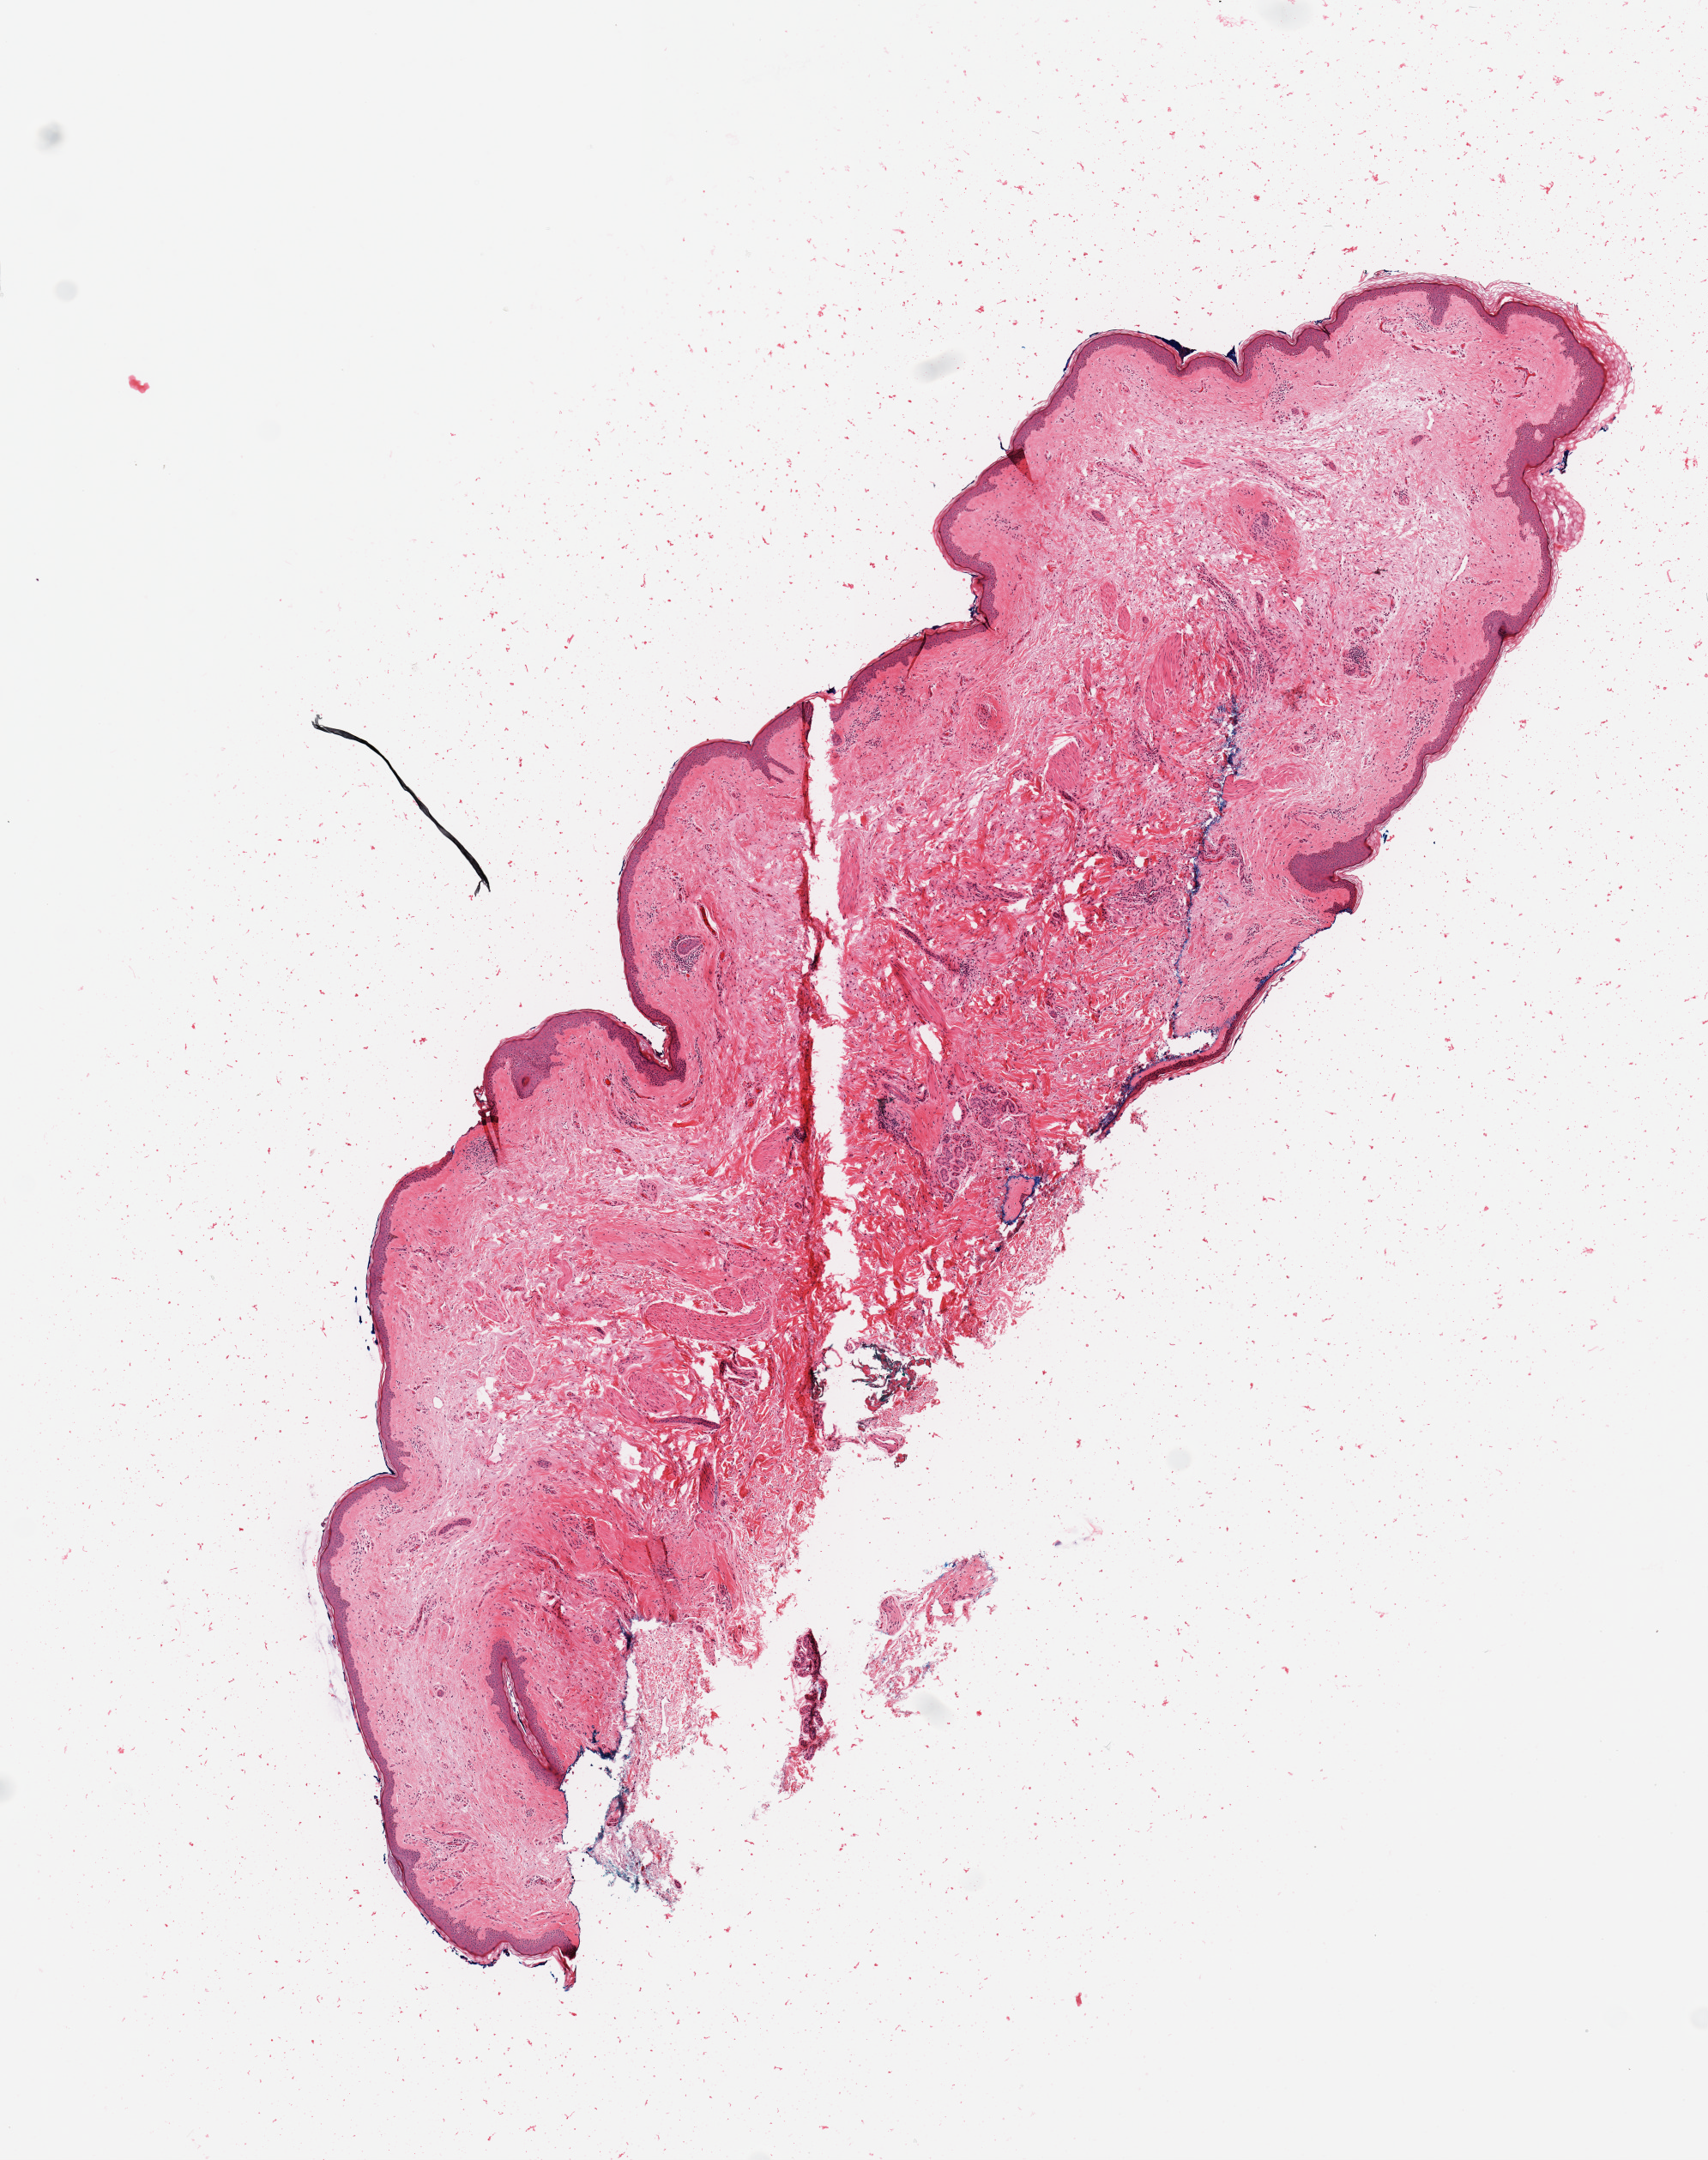
Whole-slide histology image, H&E-stained — a low-resolution overview of the entire scanned area, about 7.9 x 10.0 mm (from a 20x scan), normal (non-tumour) tissue sample. Patient sex: female.
This section: normal (non-tumour) tissue from the same patient. Patient diagnosis (cohort enrolment): sarcoma (site not recorded at cohort level).